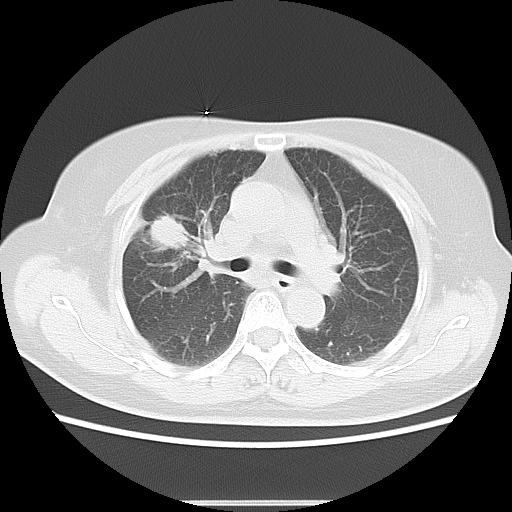
Chest CT, one axial slice; position 7 of 15 along the scan axis; lung window (W 1500 / L -600 HU); 512 × 512 image matrix. Female patient, age 57 years. Case-level facts recorded for this patient, not image findings: clinical TNM (as recorded): T1c N1 M0.
Structures marked on this image (rectangle marked by the reading radiologist):
- lung tumour (recorded histology: adenocarcinoma): bounding box (x1, y1, x2, y2) in pixels: (145, 207, 193, 257)